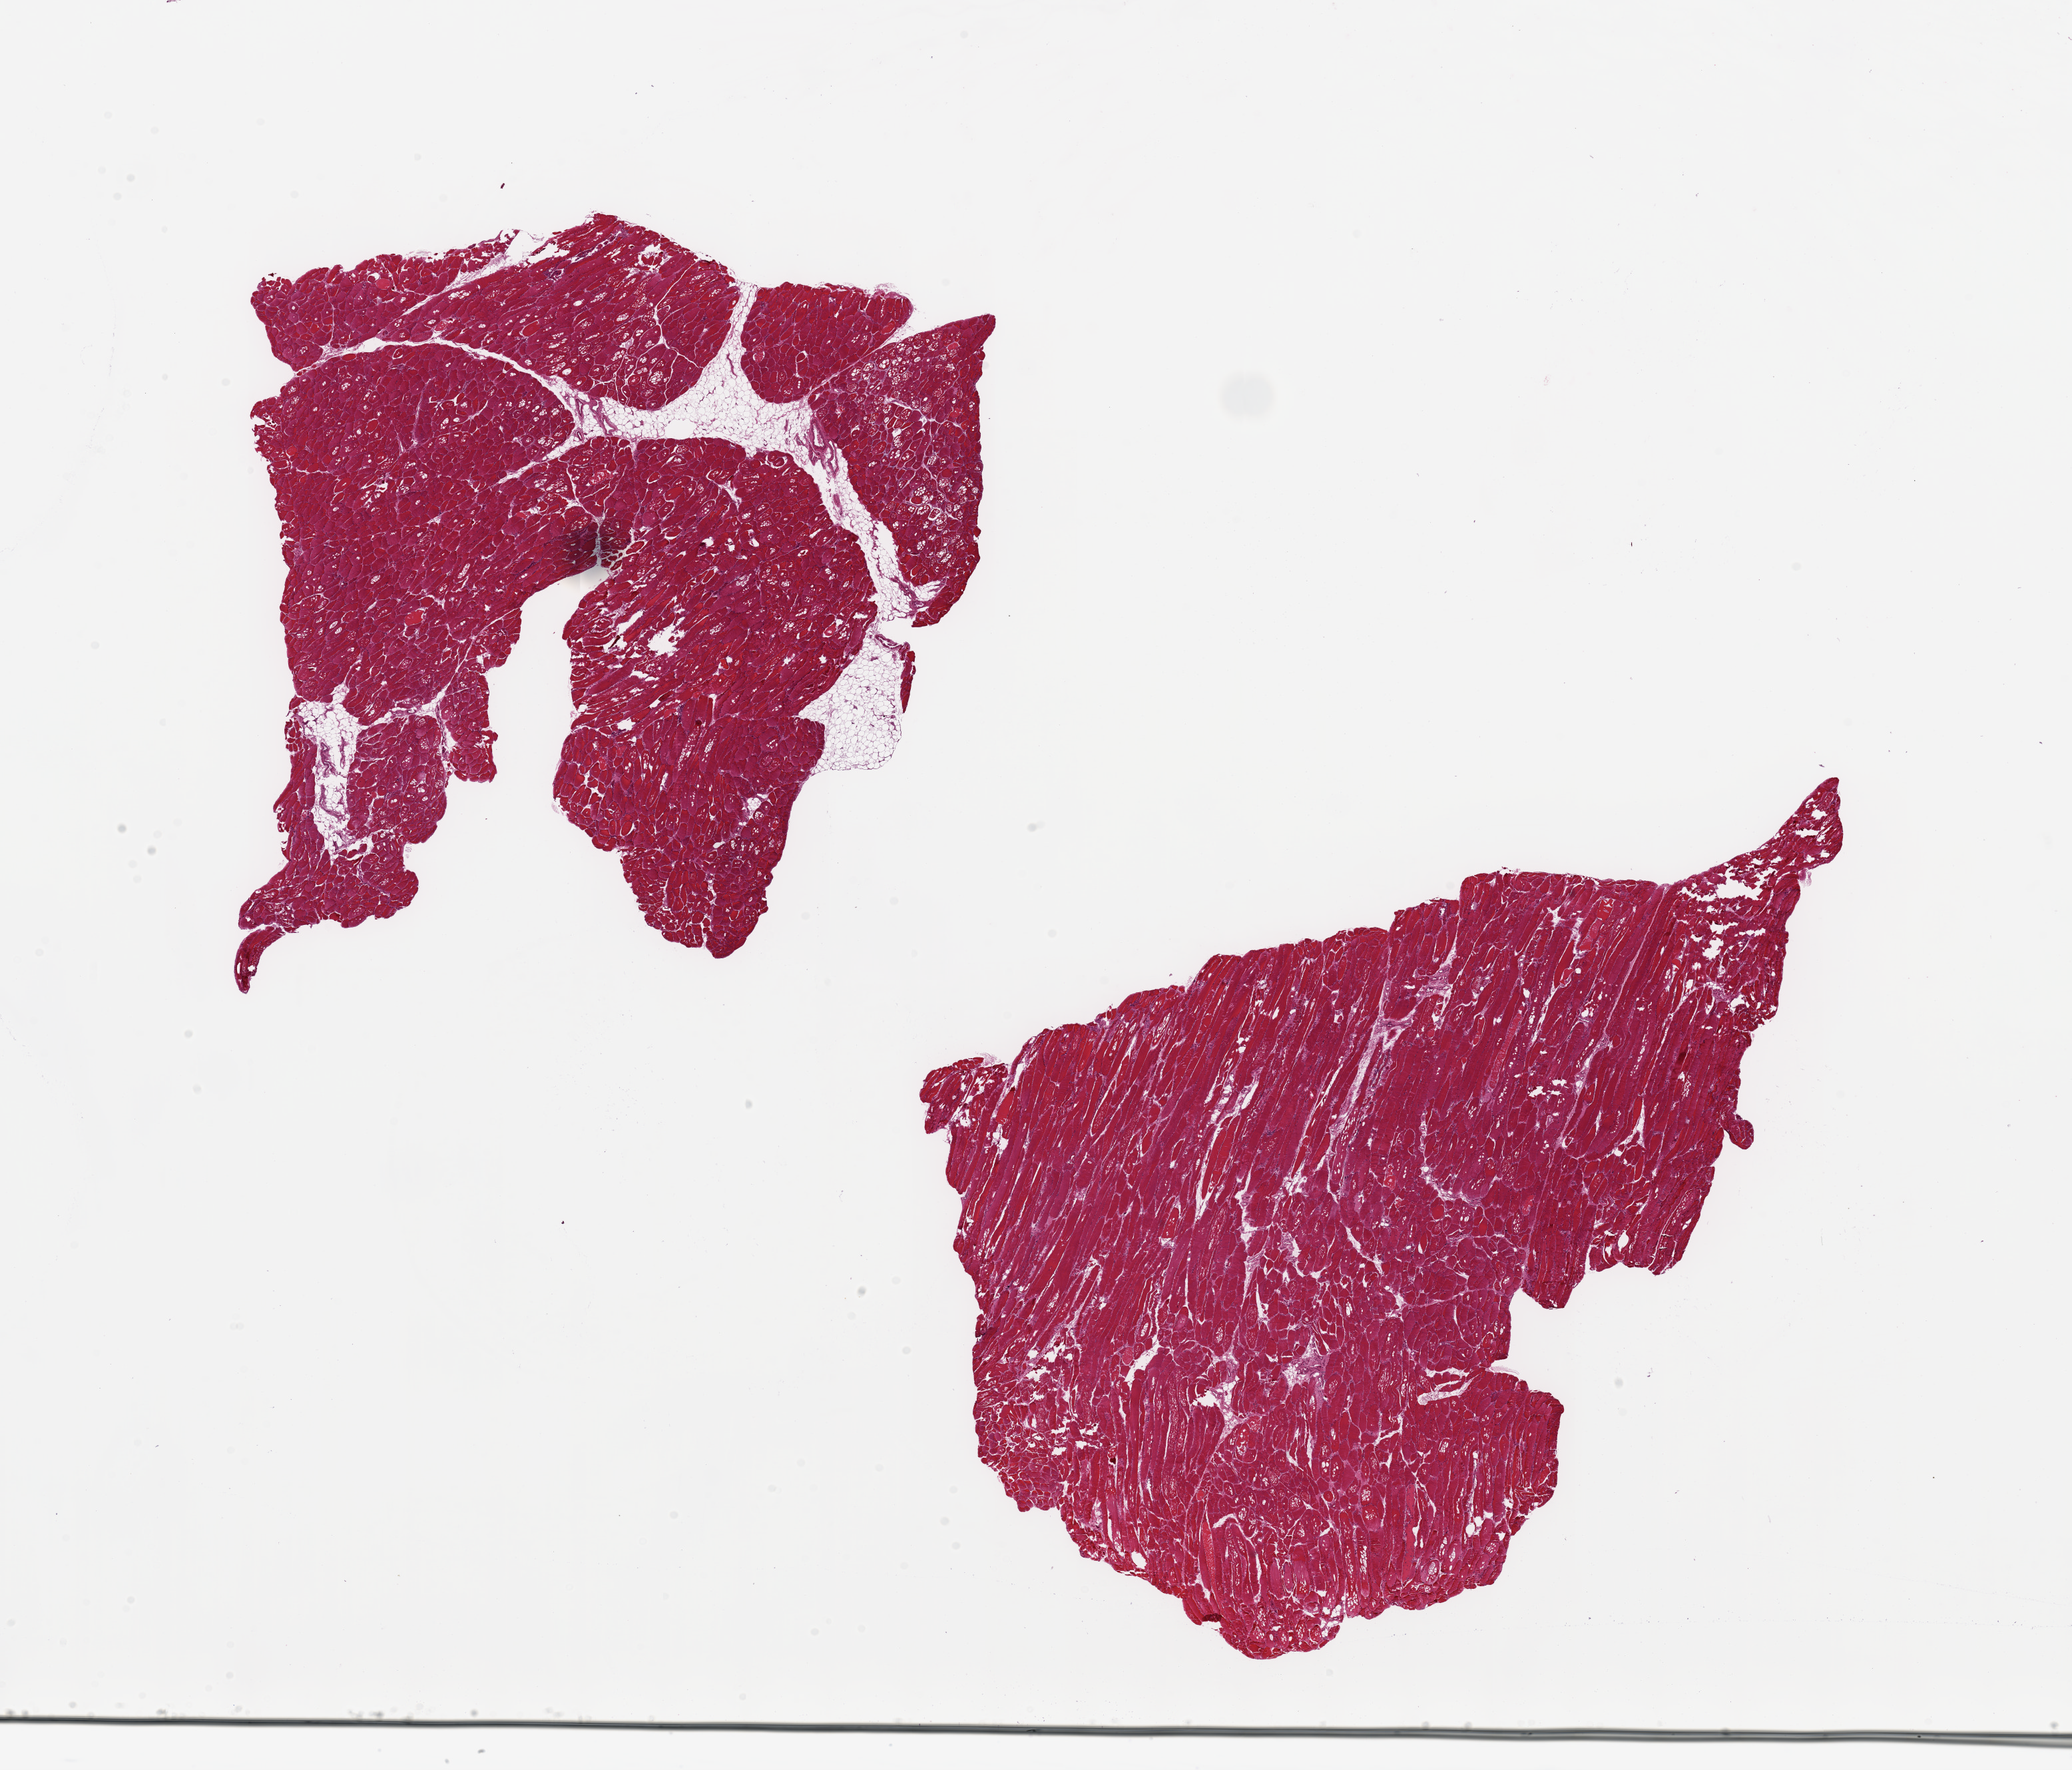
Hematoxylin and eosin (H&E) whole-slide image, brightfield, shown as a low-resolution overview of the whole scanned area (about 24.6 x 21.0 mm, slide scanned at 20x), PAXgene-fixed paraffin-embedded (PFPE) section, target tissue: skeletal muscle, tissue donor sample. Male donor.
Review note (as recorded): 2 pieces, ~ 9x7mm, areas of poor fixation.